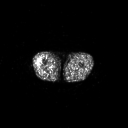
FDG PET of an extremity soft-tissue mass (from a PET/CT study), one axial slice; 3.27 mm slice thickness; 128 × 128 image matrix, field of view 700 × 700 mm. Male patient, age 43 years. Case-level facts recorded for this patient, not image findings: histological type: poorly differentiated synovial sarcoma; grade: high; site of the primary tumour: right buttock.
Annotated regions visible in this slice (expert contour drawn on MRI and transferred to this co-registered scan by the dataset authors):
- gross tumour volume including surrounding oedema: bounding box <36,60,42,67> (left, top, right, bottom; pixels)